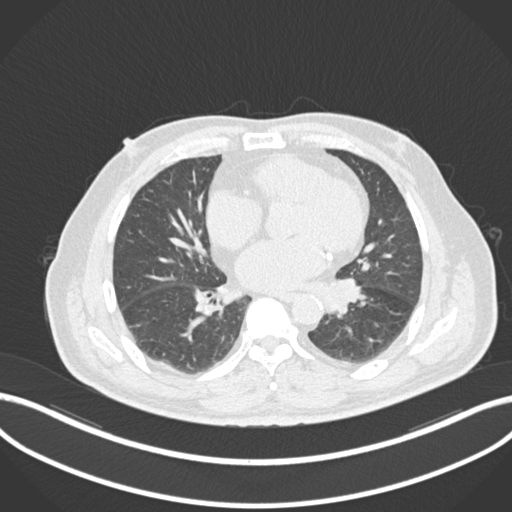
Chest CT, one axial slice; position 56 of 161 along the scan axis; reconstruction kernel B30f; lung window (W 1500 / L -600 HU); 1 mm slice thickness; 512 × 512 image matrix. Patient: male, 71 years. From the clinical record (not read from this slice): clinical TNM (as recorded): T1b N0 M0.
Annotated regions visible in this slice (rectangle marked by the reading radiologist):
- lung tumour (recorded histology: squamous cell carcinoma): box from (x=322, y=277) to (x=364, y=322) px